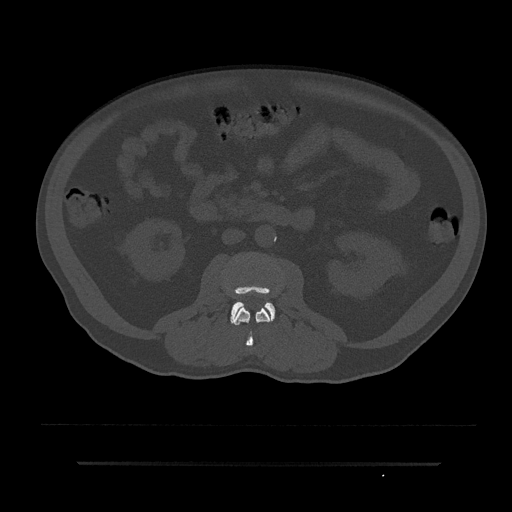
CT including the spine, one axial slice. Position 38 of 797 along the scan axis. Bone window (W 1800 / L 400 HU). 0.5 mm slice thickness. 512 × 512 image matrix, field of view 464 × 464 mm. Patient: male, 59 years. Case-level facts recorded for this patient, not image findings: primary cancer: bile ducts; vertebrae with lytic lesions (as recorded): T10.
Structures marked on this image (semi-automatic segmentation, software-assisted and operator-edited):
- L2 vertebra: bounding box [x1, y1, x2, y2] px = [233, 306, 272, 347]
- L3 vertebra: [230, 287, 275, 324]